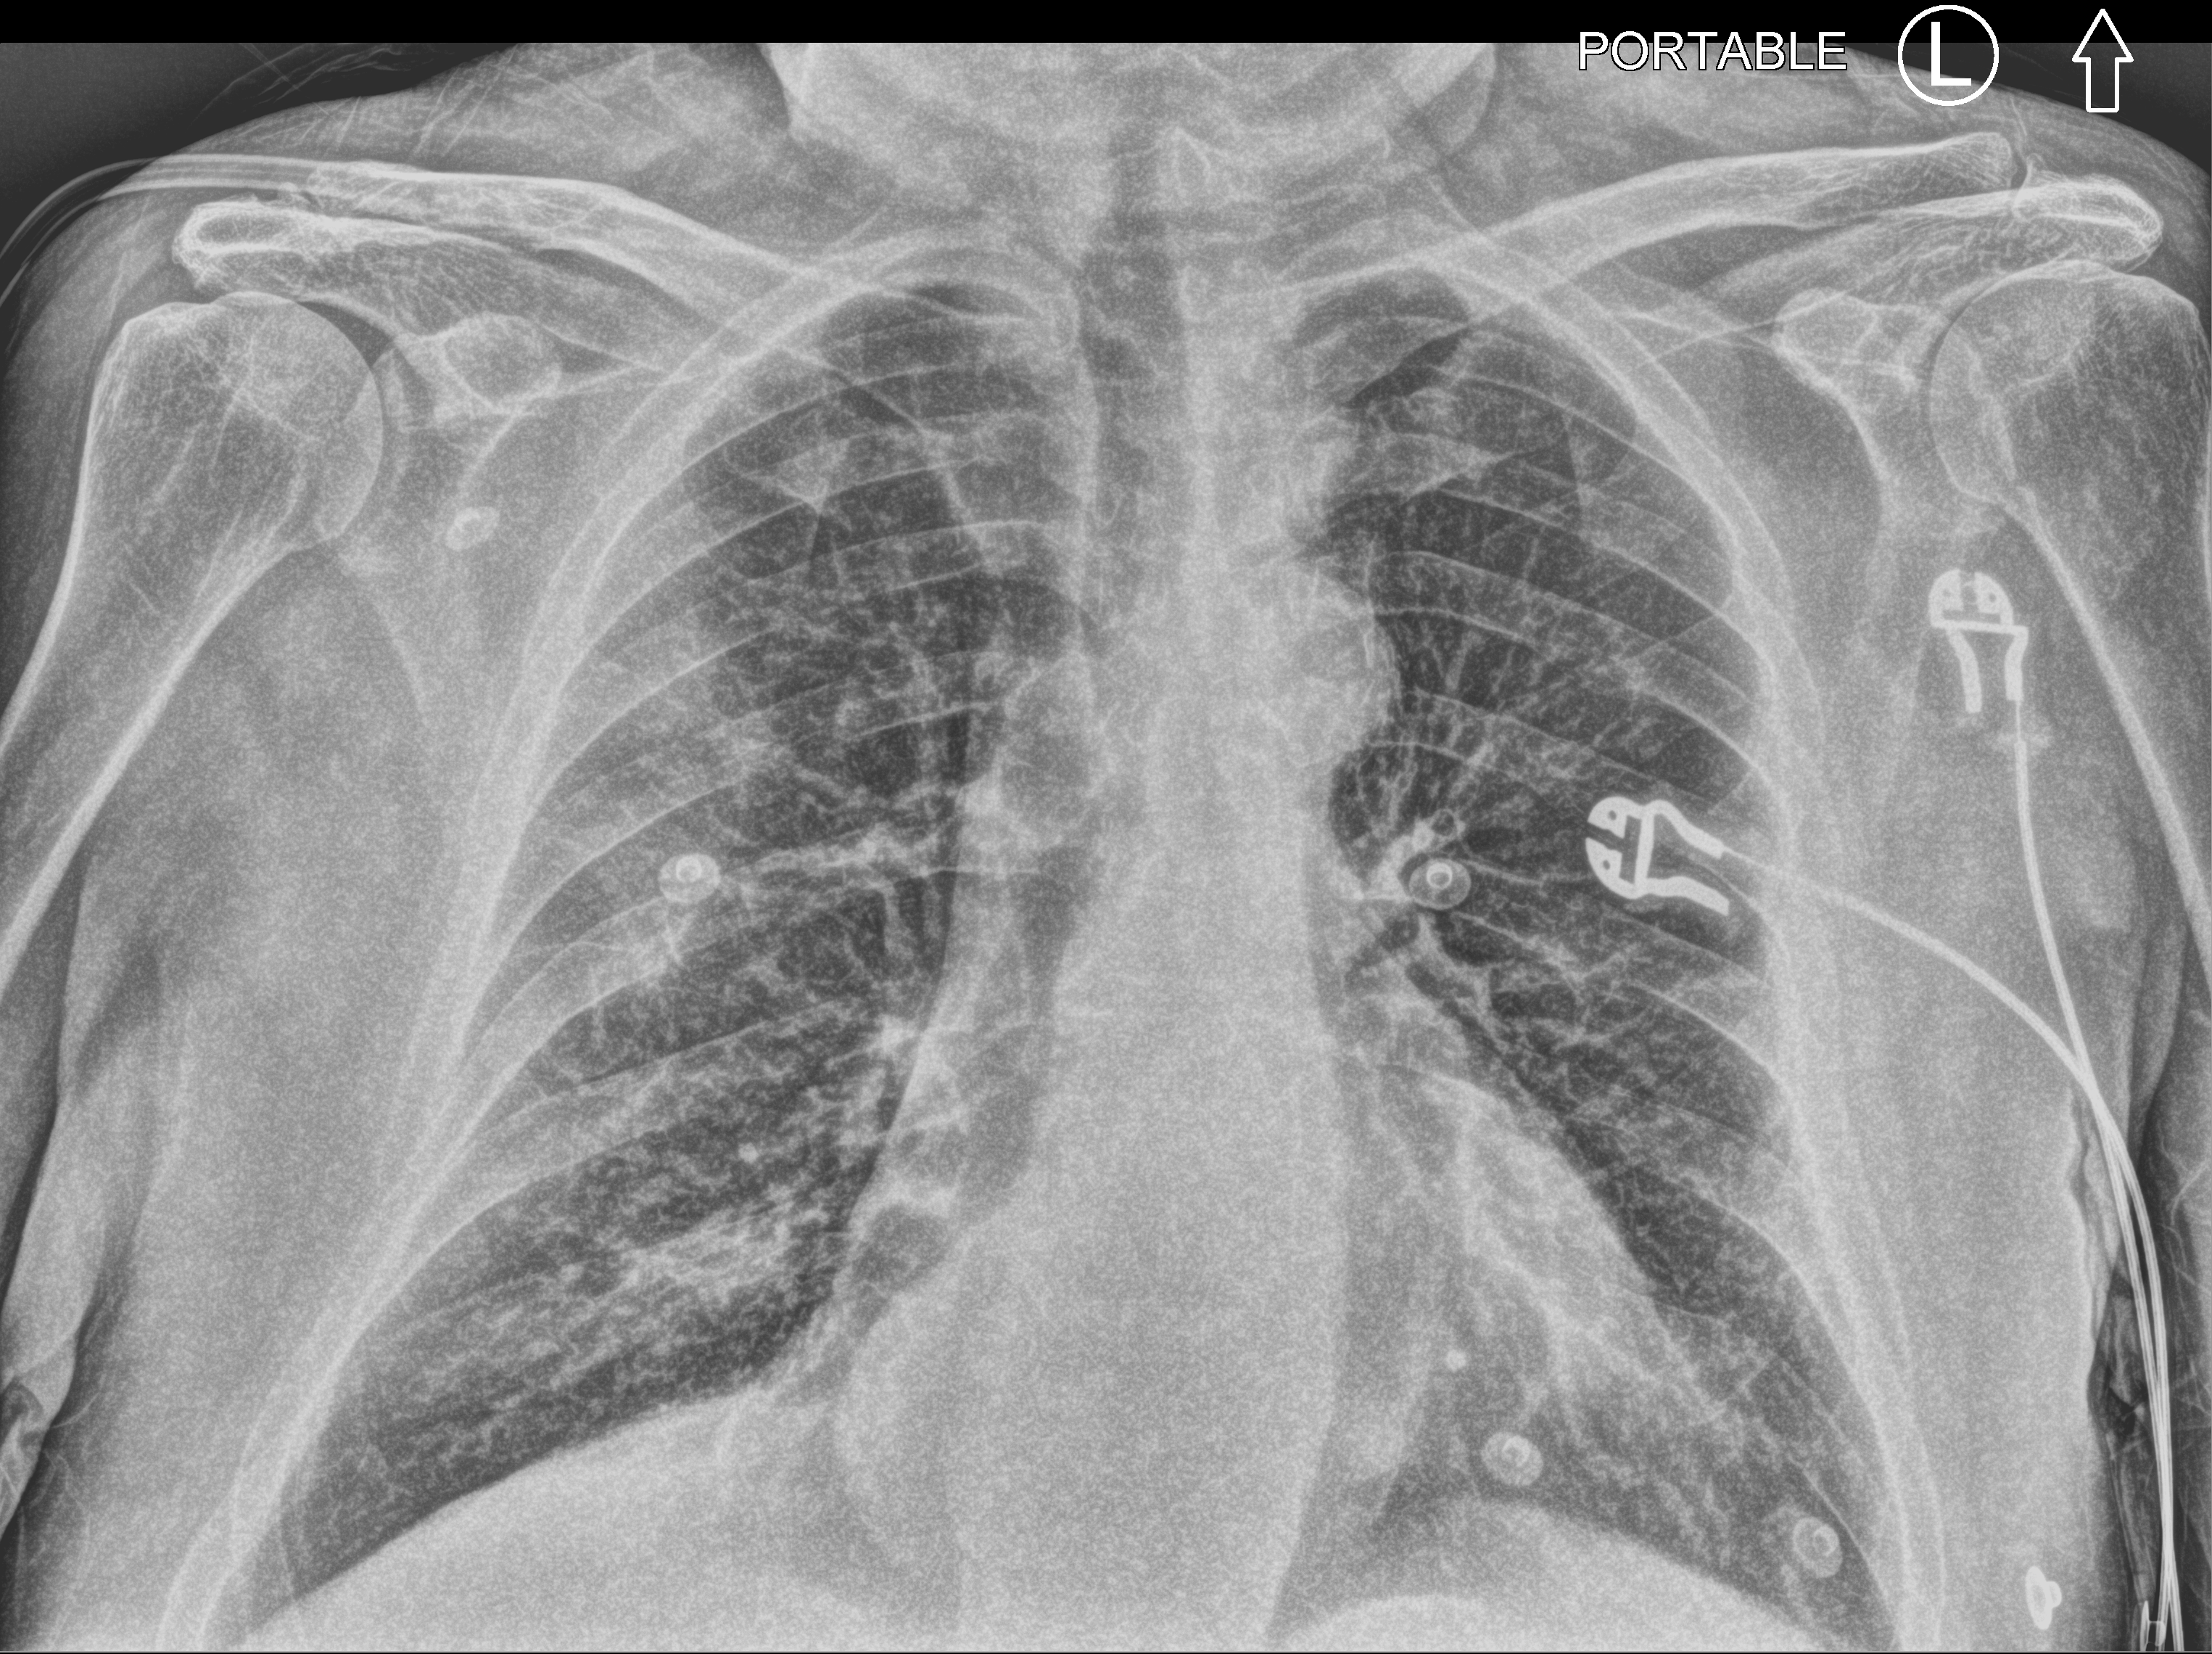
Bedside chest radiograph (computed radiography), anteroposterior (AP) projection. Male patient hospitalised with COVID-19, age 75–90 years.
Hospital-stay facts (about this admission, not read from this image; timing relative to this image not recorded):
- mechanically ventilated during this hospital stay: no
- hypertension (admission record): yes
- admitted to intensive care during this hospital stay: no